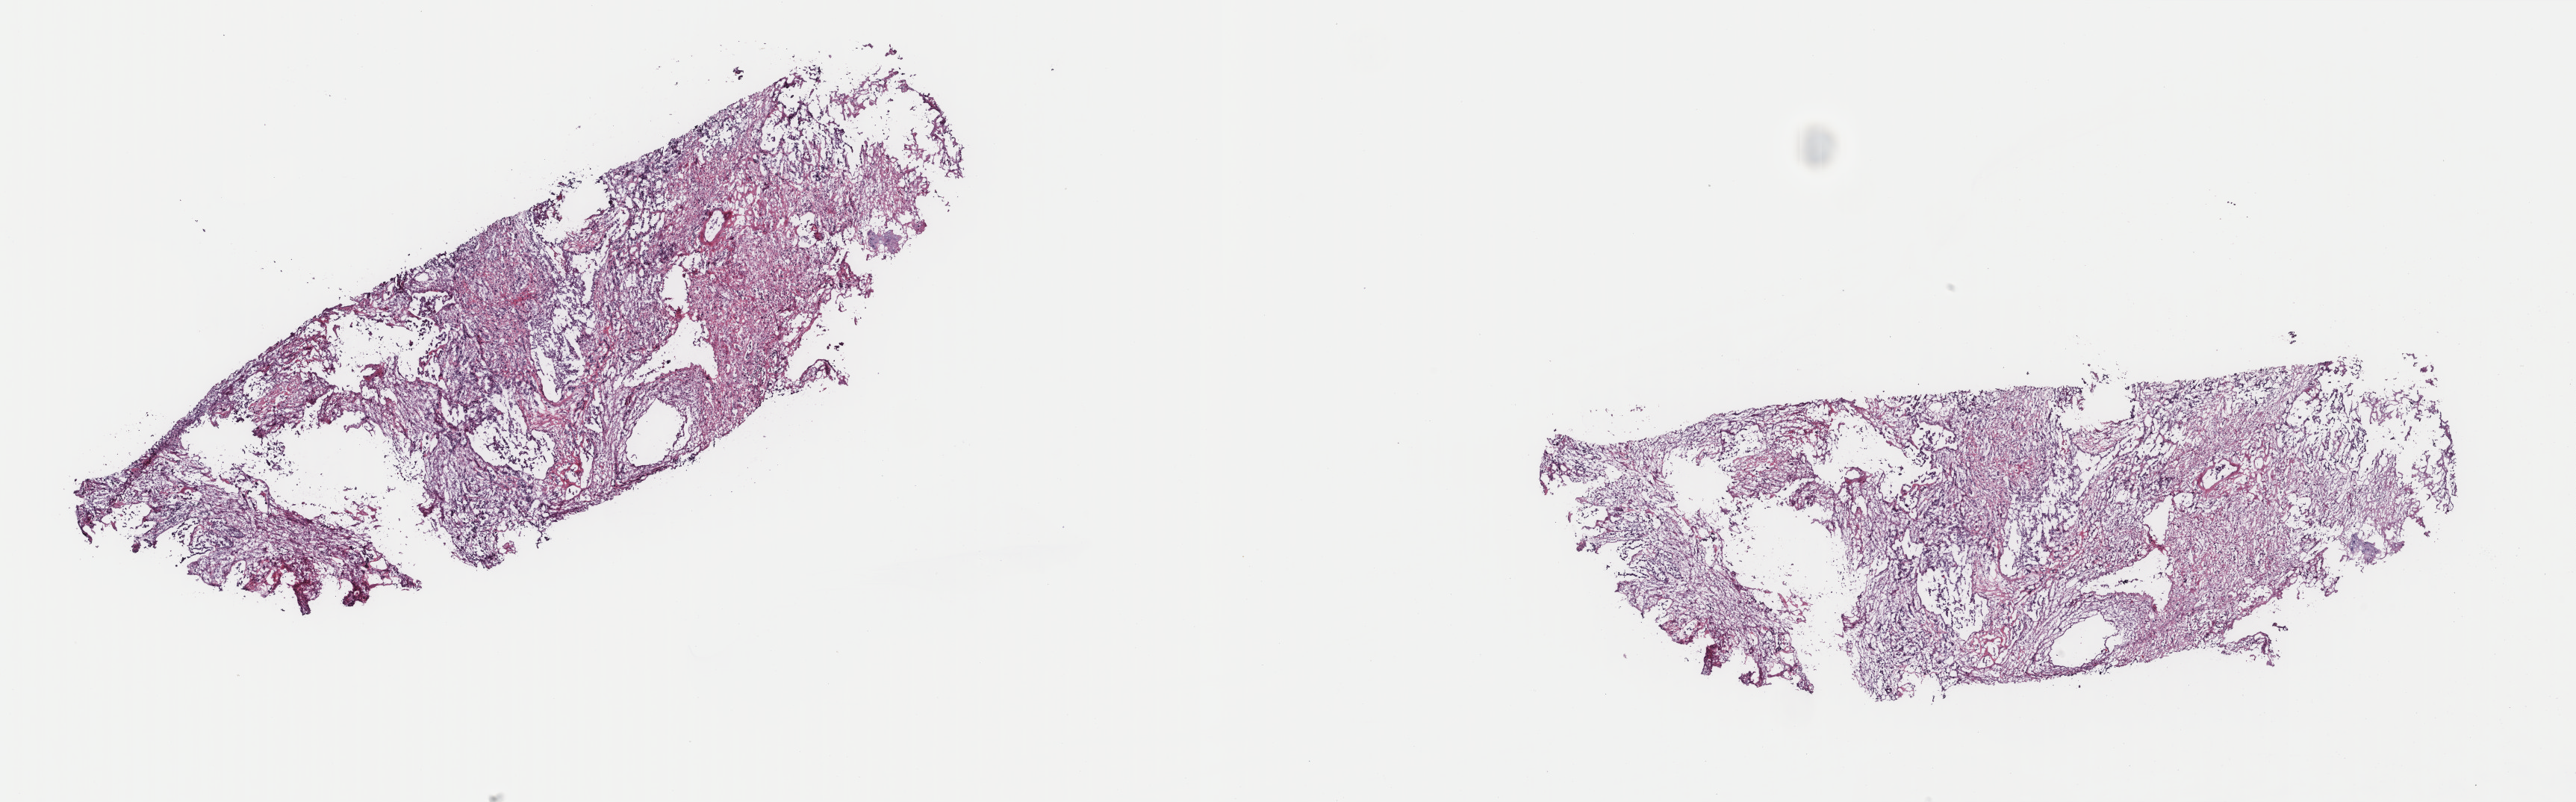
Whole-slide histology image, H&E, shown as a low-resolution overview of the whole scanned area (about 27.4 x 8.5 mm, slide scanned at 40x), frozen section, sample: primary tumour, uterus. Female, age 80 years at initial diagnosis. Pathologist review of this section (percent, as recorded): tumour cells 70%, tumour nuclei 70%, normal cells 0%, stromal cells 10%, necrosis 20%. Inflammatory infiltration, as recorded: lymphocyte infiltration 20%, monocyte infiltration 20%, neutrophil infiltration 40%.
- FIGO stage: IIIB
- pathologic diagnosis: Carcinosarcoma, NOS